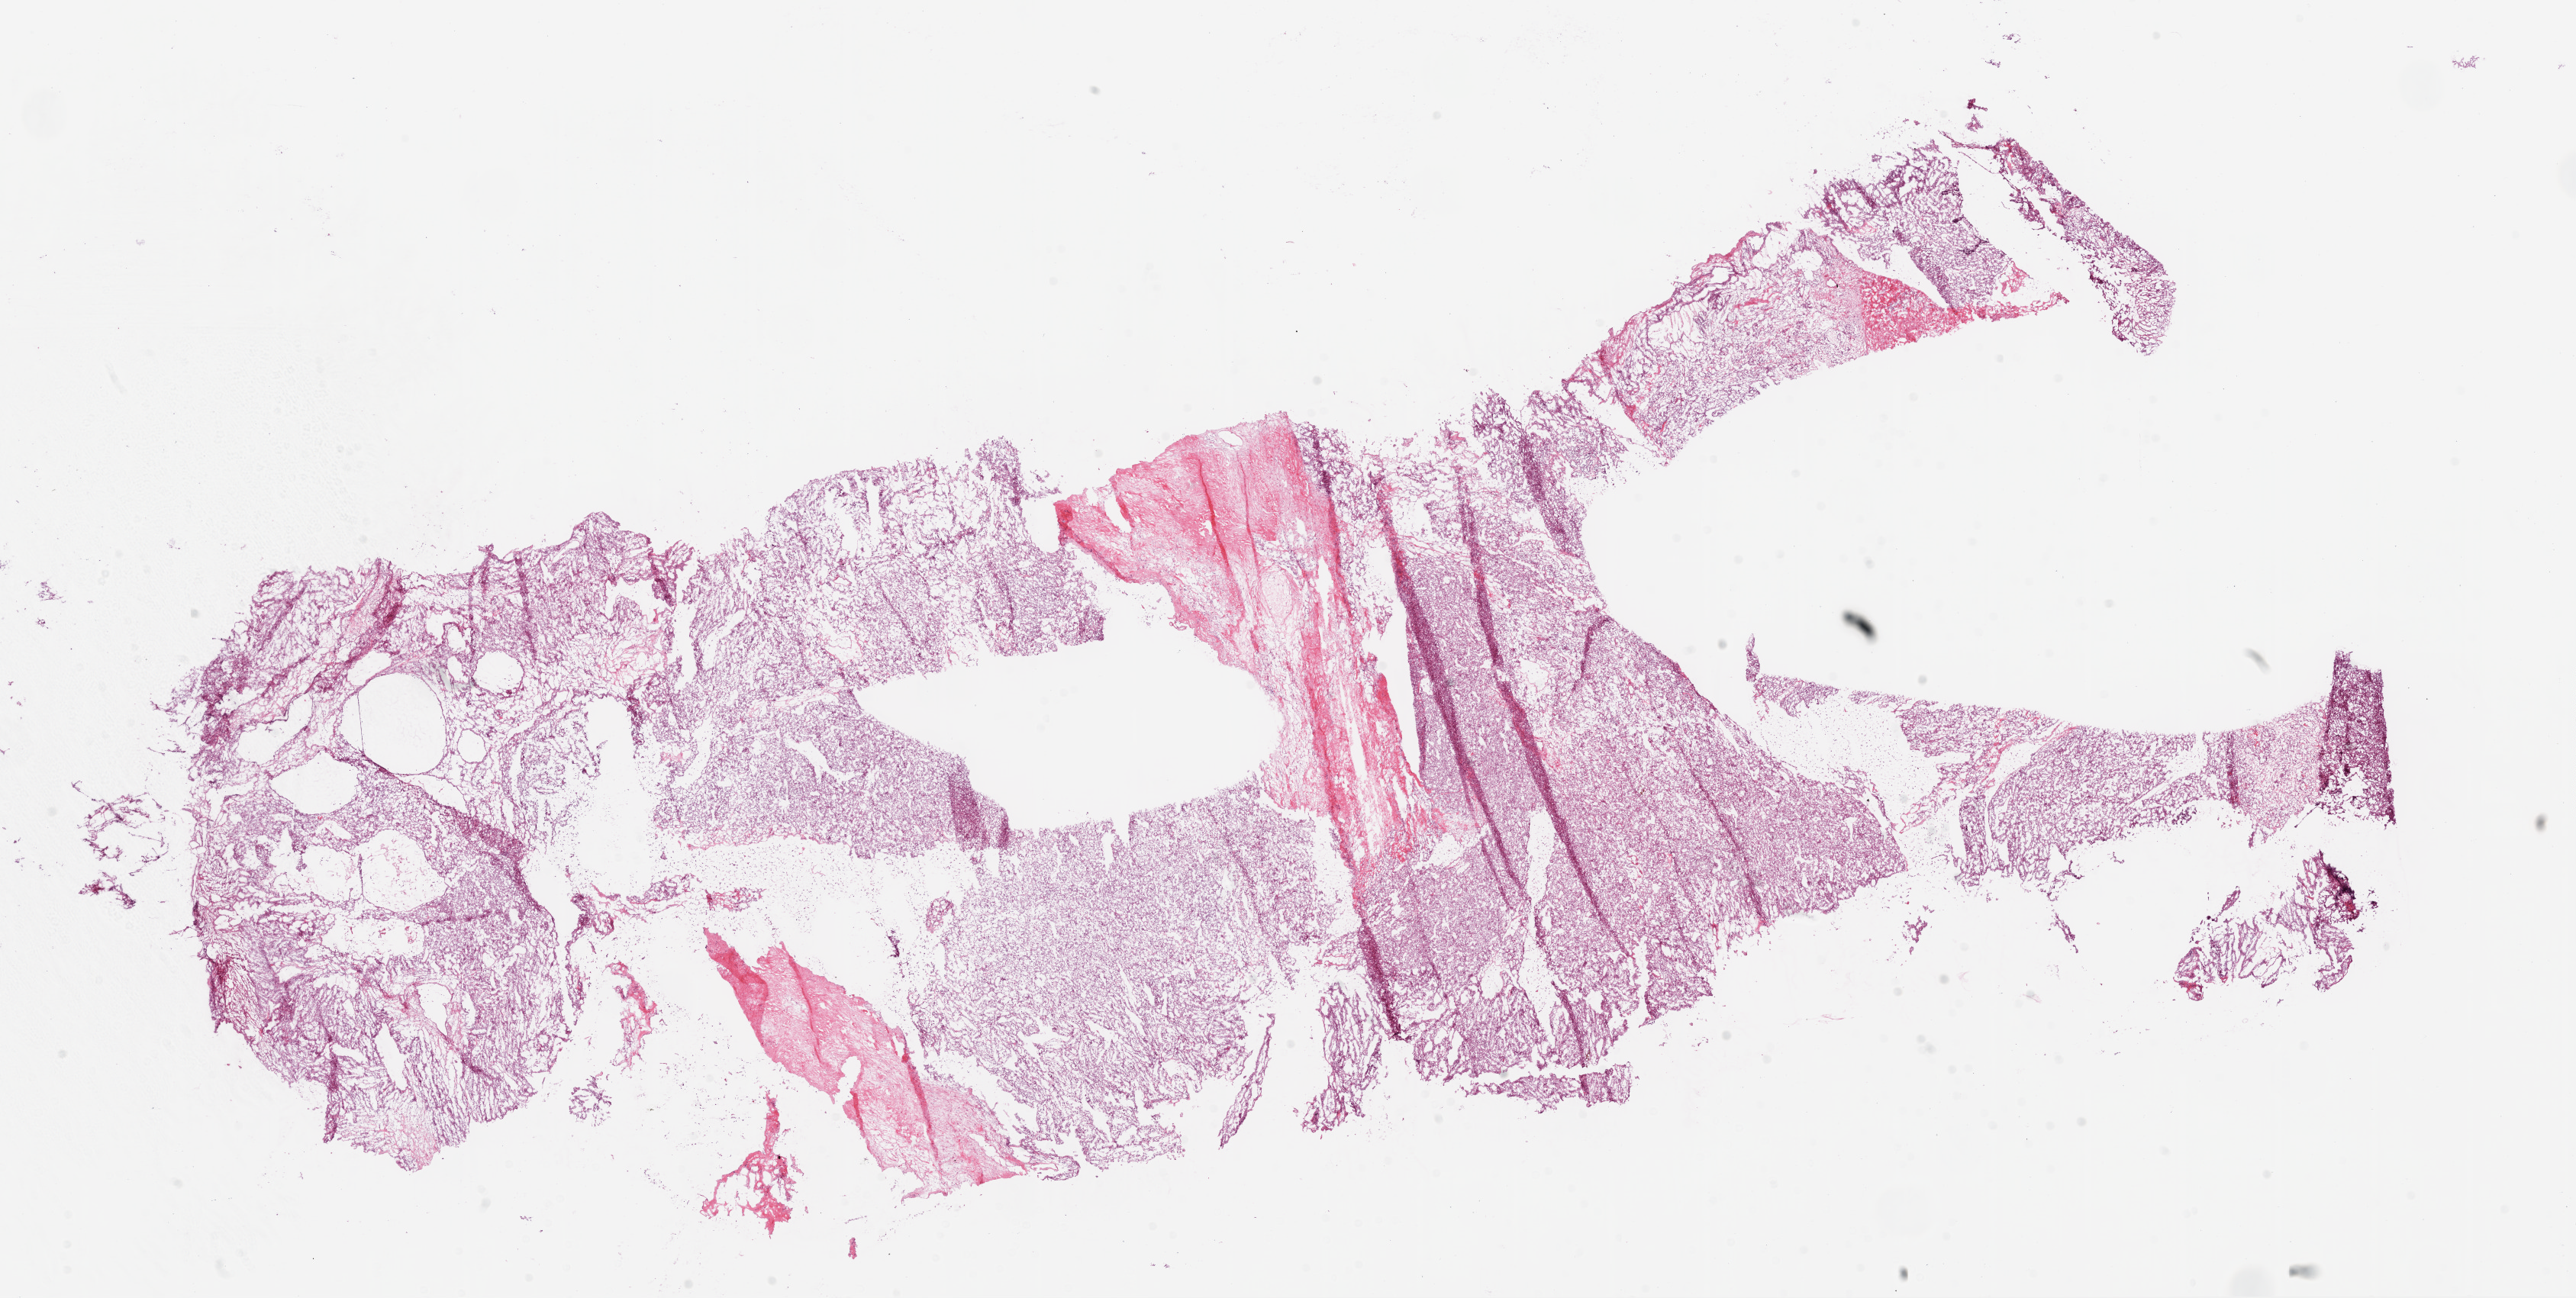
Hematoxylin and eosin (H&E) stained whole-slide image, low-resolution overview of the scanned area, about 27.1 x 13.6 mm (from a 20x scan). Frozen section. Sample: primary tumour, kidney. Patient: male, age at initial diagnosis 49 years. Histologic grade: G4 (undifferentiated). Slide review estimates, as recorded: tumour cells 80%, tumour nuclei 80%, normal cells 0%, stromal cells 20%, necrosis 0%.
- diagnosis: Clear cell adenocarcinoma, NOS
- TNM: T3a N0 M0
- AJCC pathologic stage: III (7th edition)